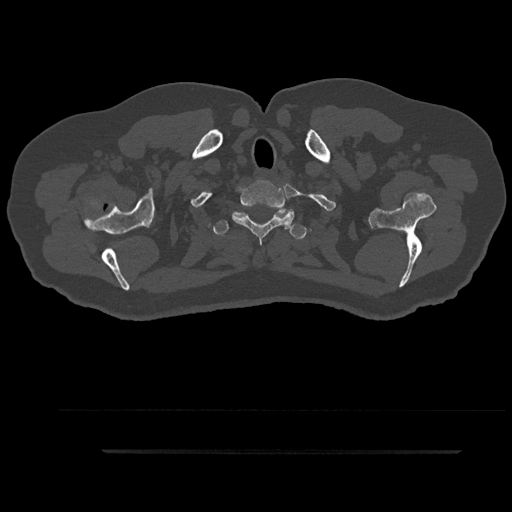
CT including the spine, one axial slice. 120 kVp. Bone window (W 1800 / L 400 HU). 0.5 mm slice thickness. 512 × 512 image matrix, field of view 432 × 432 mm. Patient: male, 63 years. From the clinical record (not read from this slice): primary cancer: renal; vertebrae with lytic lesions (as recorded): T8.
Structures marked on this image (semi-automatically segmented with operator editing):
- T1 vertebra: bounding box [x1, y1, x2, y2] px = [232, 185, 294, 244]
- T2 vertebra: [212, 208, 306, 240]